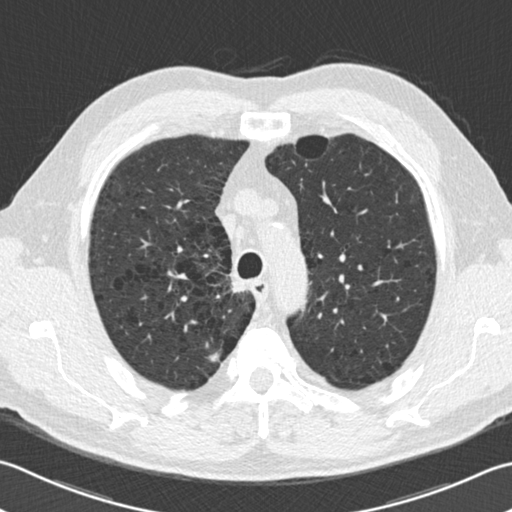
Axial slice from a low-dose chest CT screening exam. Second screening round (one year after baseline). Lung window (W 1500 / L -600 HU). 512 × 512 image matrix. Male, age 68 years at enrolment.
Expert reader's lesion annotation, box from (x=198, y=341) to (x=228, y=370) px. Screening reader's record for this exam (one nodule recorded; not confirmed to be the boxed lesion): non-calcified nodule or mass ≥4 mm, right upper lobe, 30 × 20 mm, smooth margins, pre-existing on the prior screen: no. Participant outcome: lung cancer diagnosed 414 days after this screen — adenocarcinoma, NOS, right upper lobe, well differentiated (G1), stage IB (AJCC 6th edition), 15 mm at pathology.